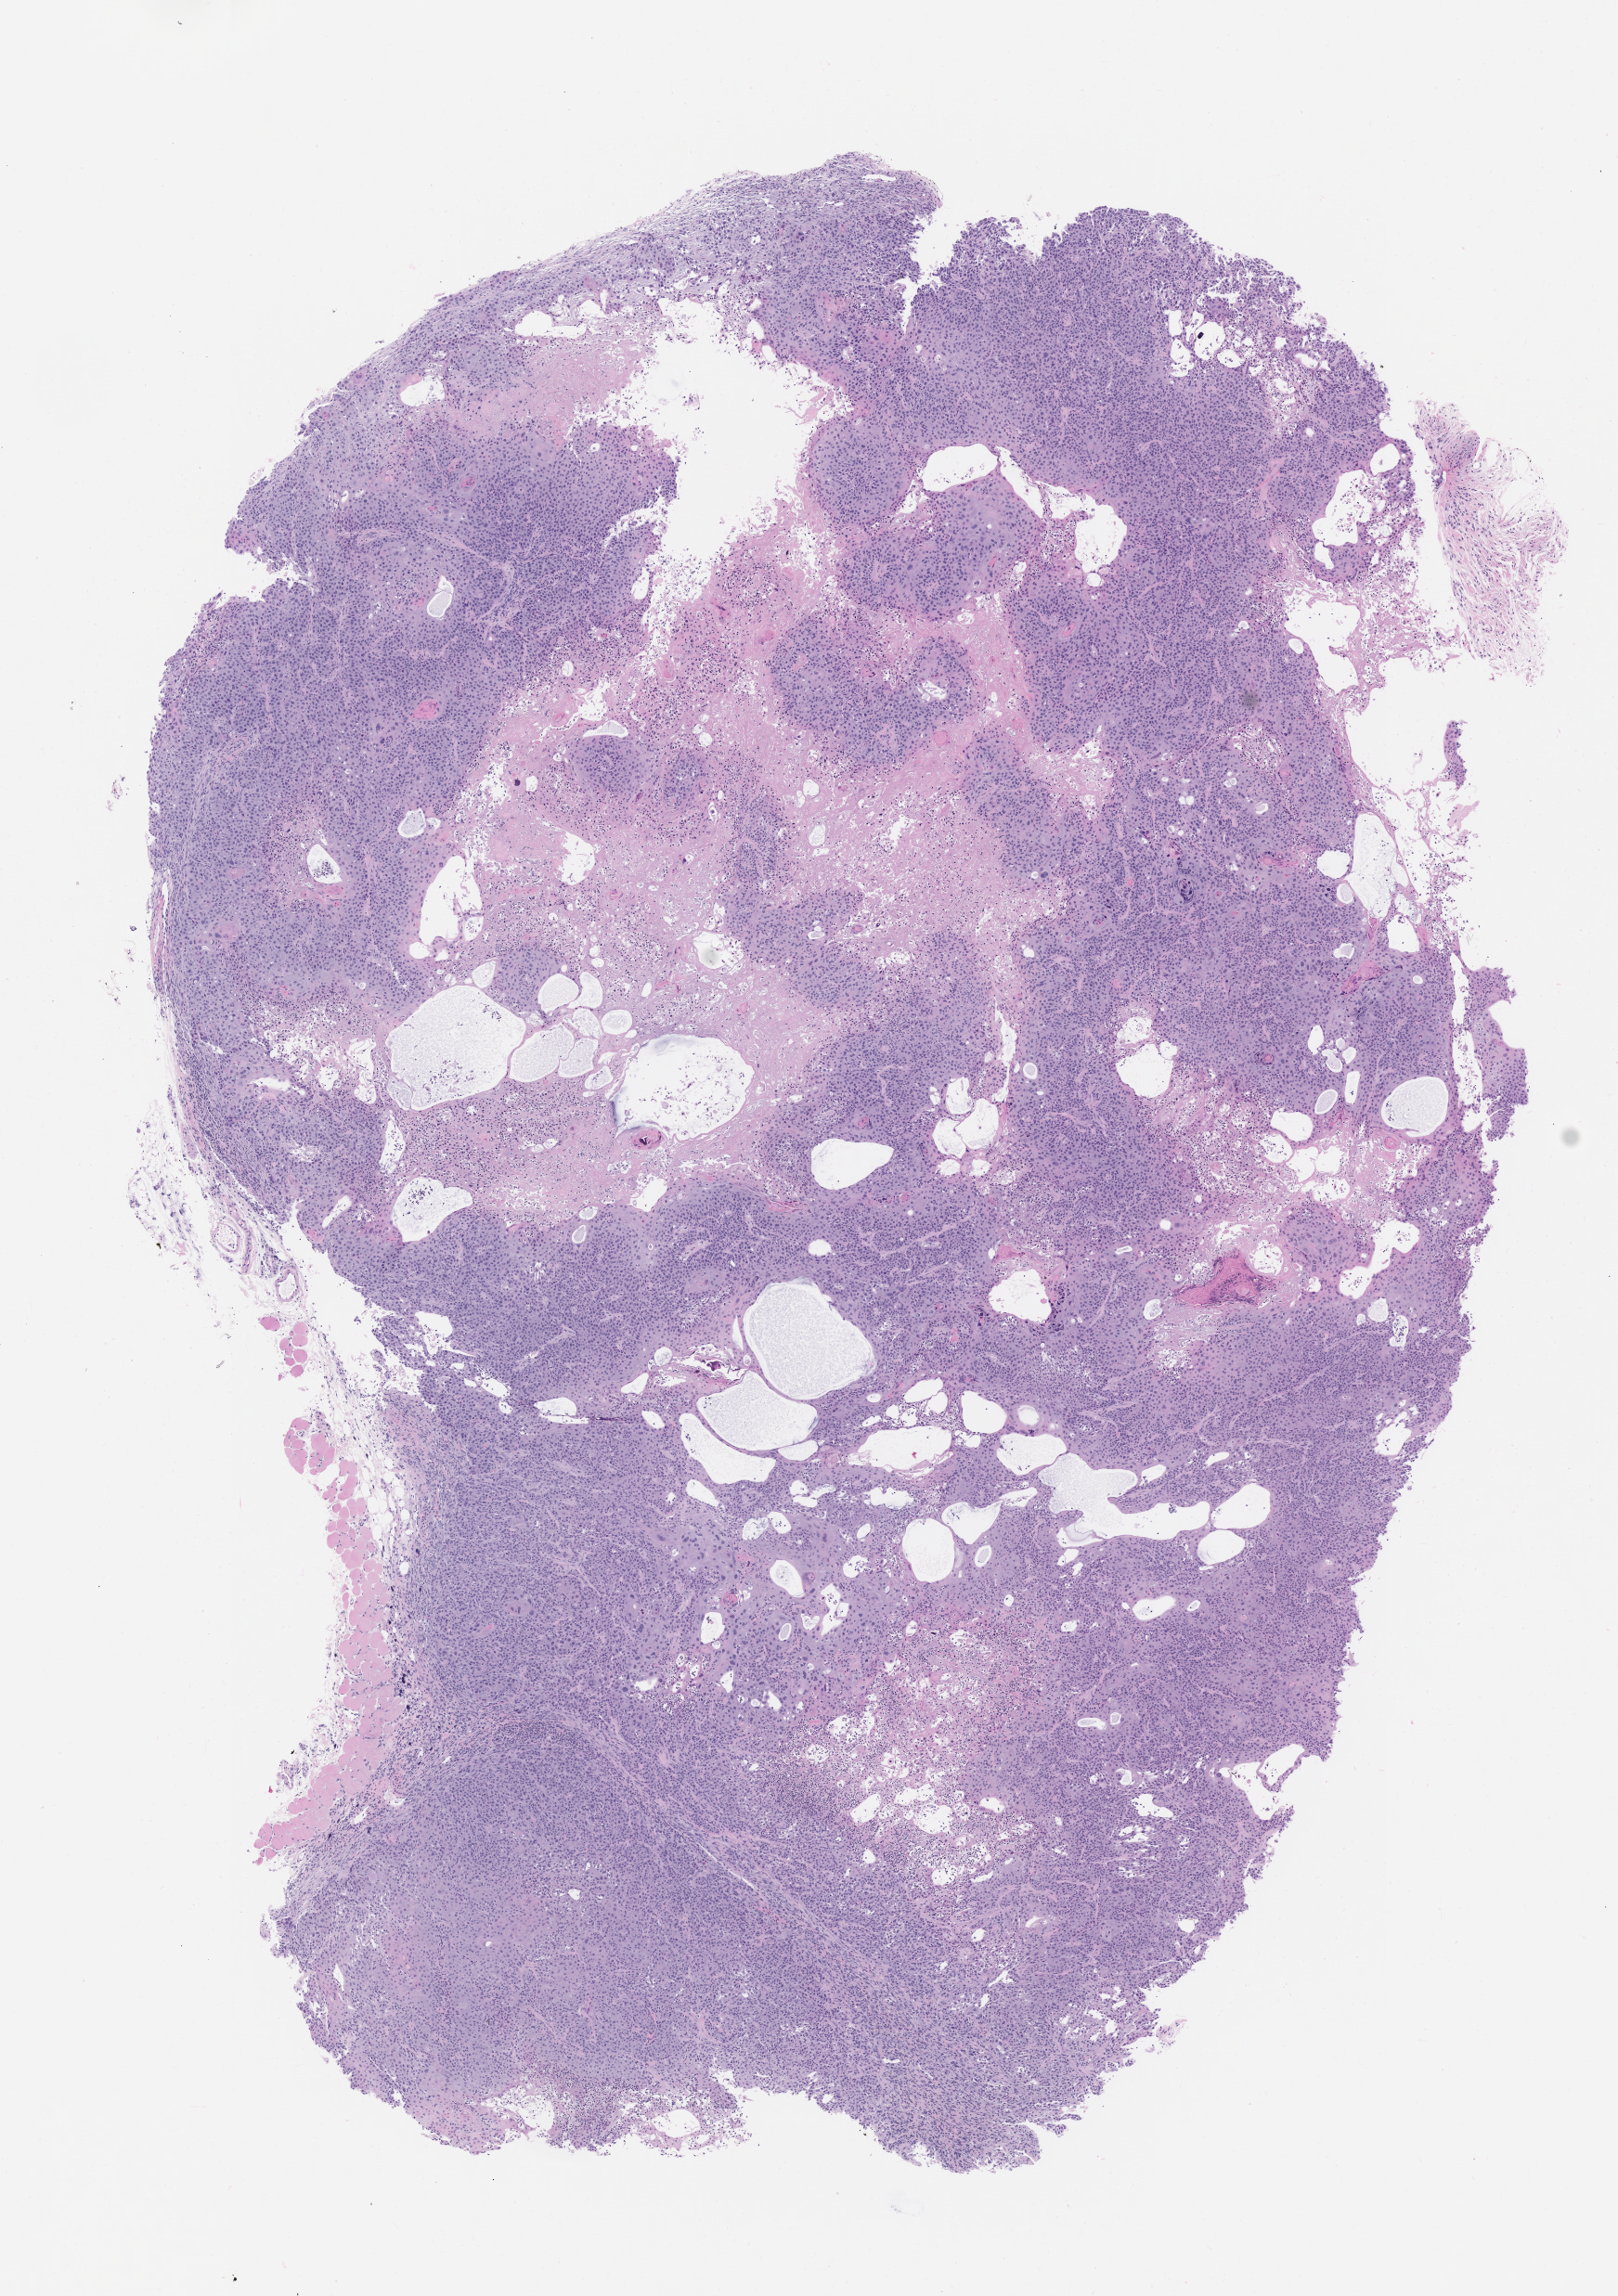
Whole-slide image, H&E: patient-derived xenograft (human tumor grown in a mouse), passage 1 — shown as a low-resolution overview of the whole scanned area (about 7.0 x 9.9 mm), formalin-fixed paraffin-embedded section, tumor site category: head and neck.
Originating patient diagnosis: Mucoepidermoid Carcinoma.